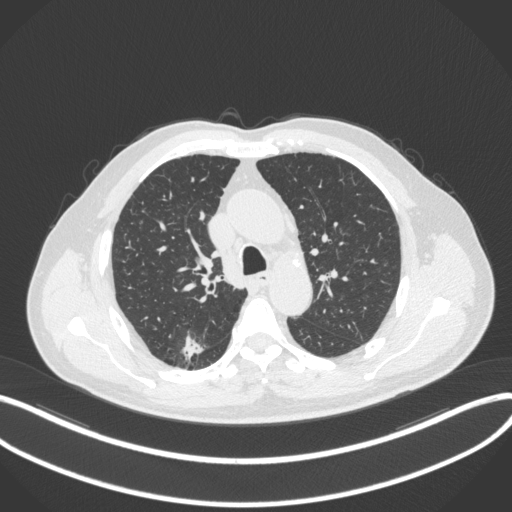
Chest CT, one axial slice. Slice 259 of 366 in the series (ordered by position). Lung window (W 1500 / L -600 HU). 1 mm slice thickness. 512 × 512 image matrix, field of view 400 × 400 mm. Patient: male, 69 years. From the clinical record (not read from this slice): clinical TNM (as recorded): T1b N0 M0; histopathological grade: G2-3.
Annotated regions visible in this slice (bounding box drawn by a radiologist):
- lung tumour (recorded histology: adenocarcinoma): bounding box <178,332,205,367> (left, top, right, bottom; pixels)